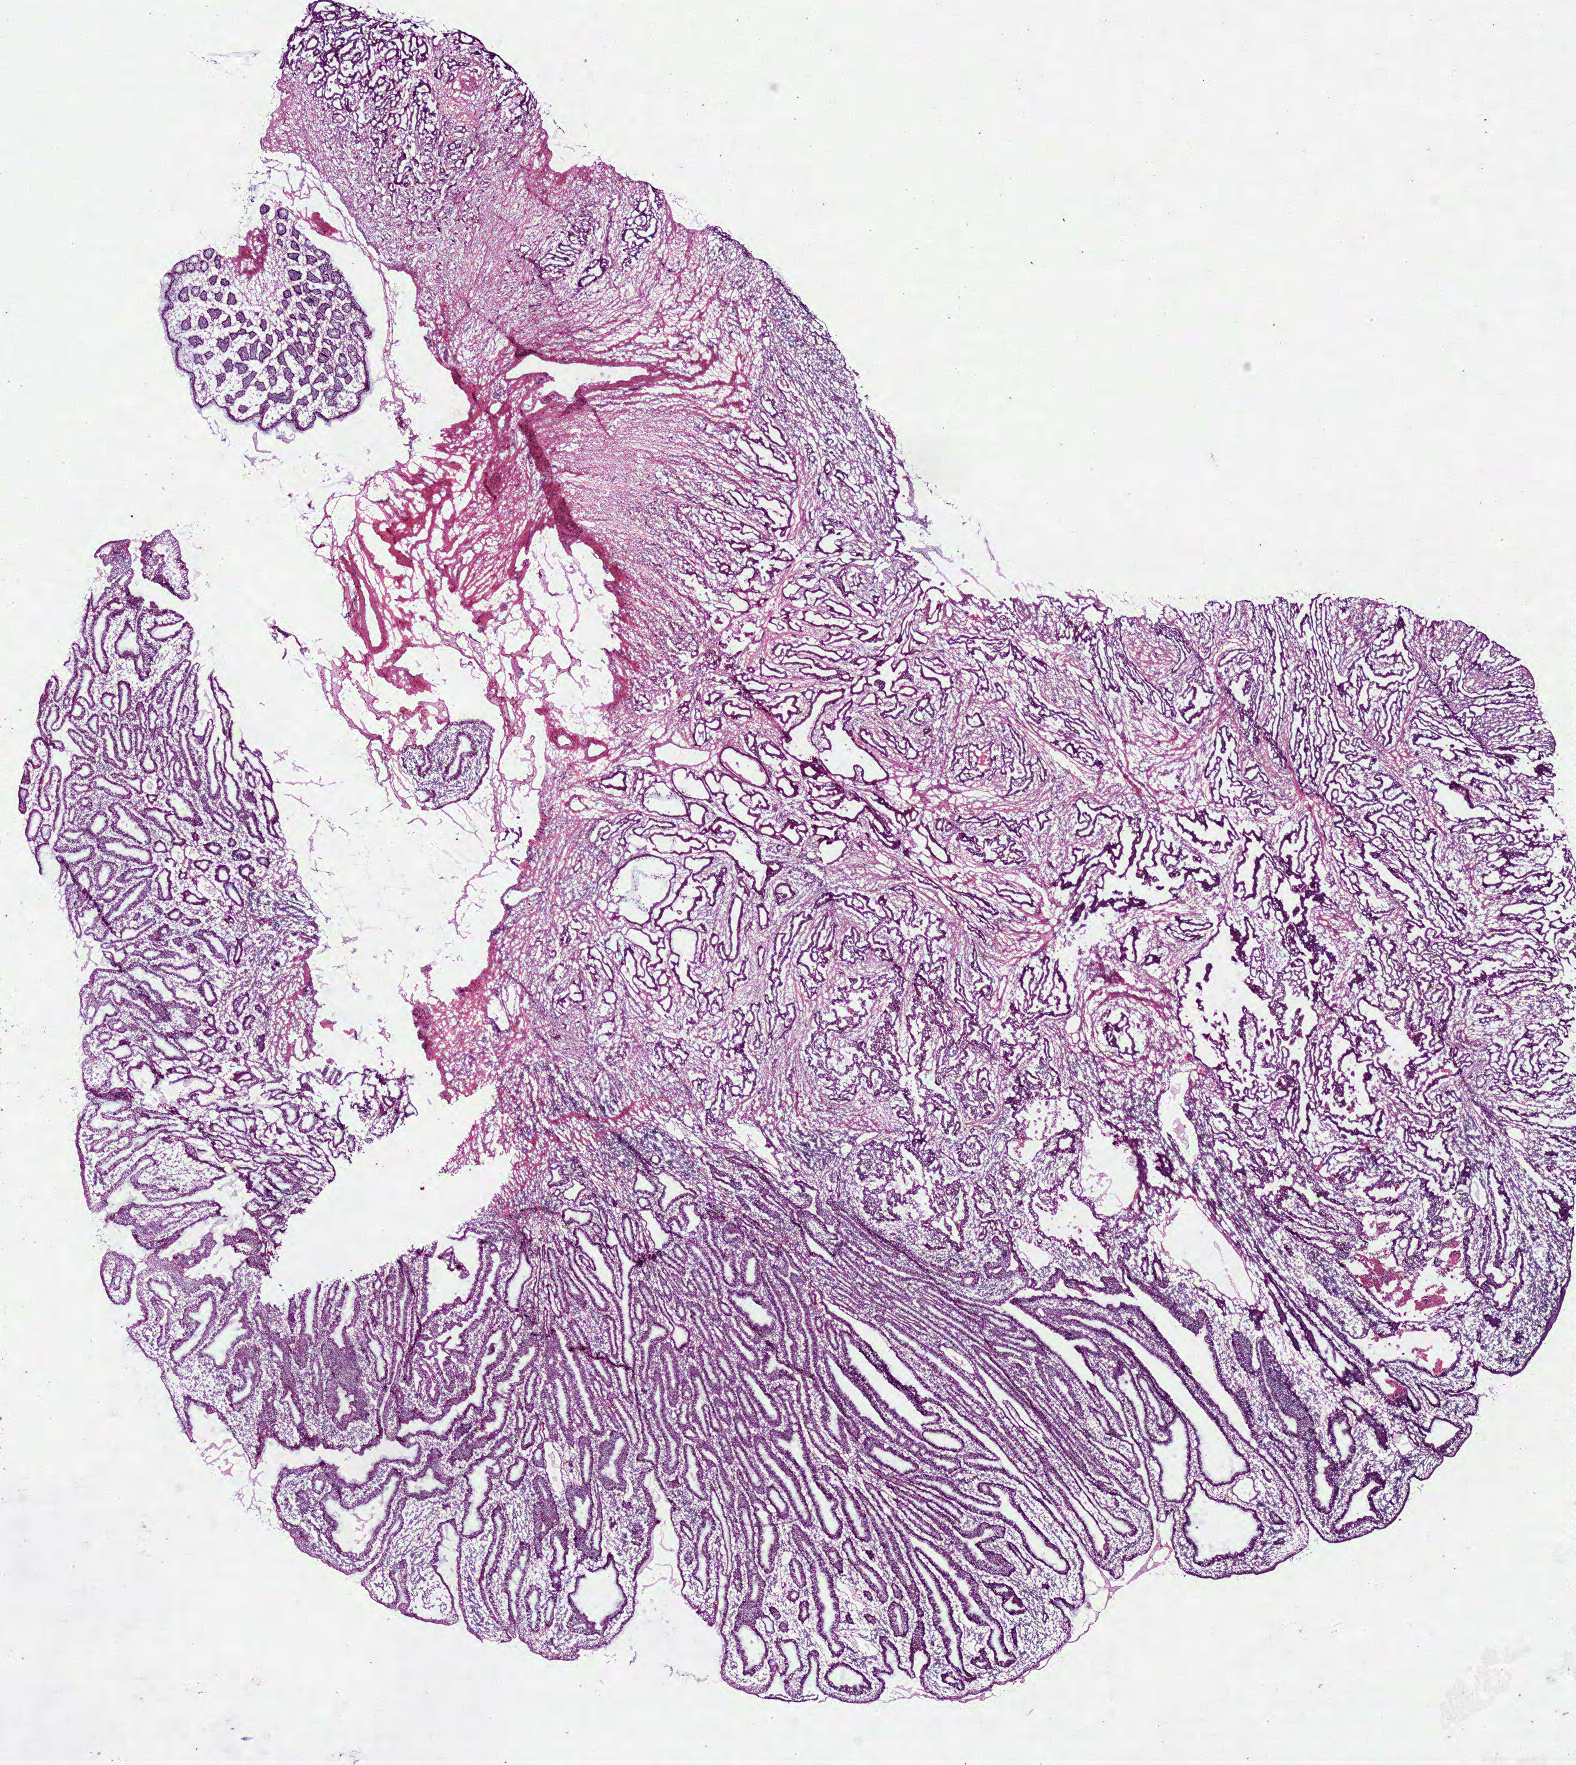
Hematoxylin and eosin (H&E) stained whole-slide image, a low-resolution overview of the entire scanned area, about 12.4 x 13.9 mm. Frozen section from the bottom of the tissue portion. Colon, primary tumour sample. Female, age 59 years at initial diagnosis. Composition of this section per pathologist review: tumour cells 82%, tumour nuclei 80%, normal cells 3%, stromal cells 10%, necrosis 5%.
• AJCC pathologic stage: I (7th edition)
• pathologic diagnosis: Adenocarcinoma, NOS (sigmoid colon)
• lymph nodes positive (case pathology): 0 of 5 examined